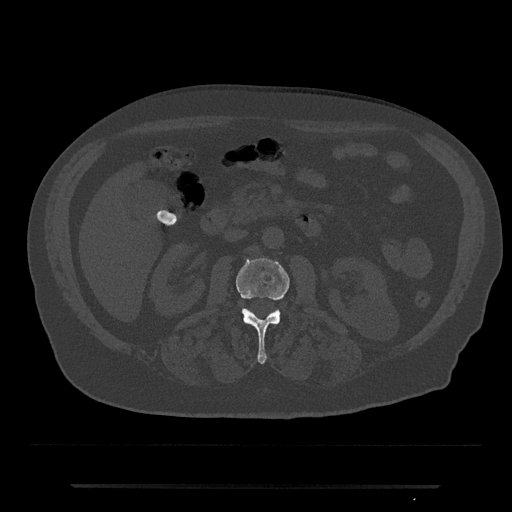
CT including the spine, one axial slice. Slice 464 of 797 in the series (ordered by position). Reconstruction kernel Br40s/3. Bone window (W 1800 / L 400 HU). 0.5 mm slice thickness. 512 × 512 image matrix, field of view 434 × 434 mm. Patient: male, 80 years. From the clinical record (not read from this slice): primary cancer: prostate; vertebrae with lytic lesions (as recorded): L1, T11.
Structures marked on this image (semi-automatically segmented with operator editing):
- L2 vertebra: bounding box <236,258,290,363> (left, top, right, bottom; pixels)